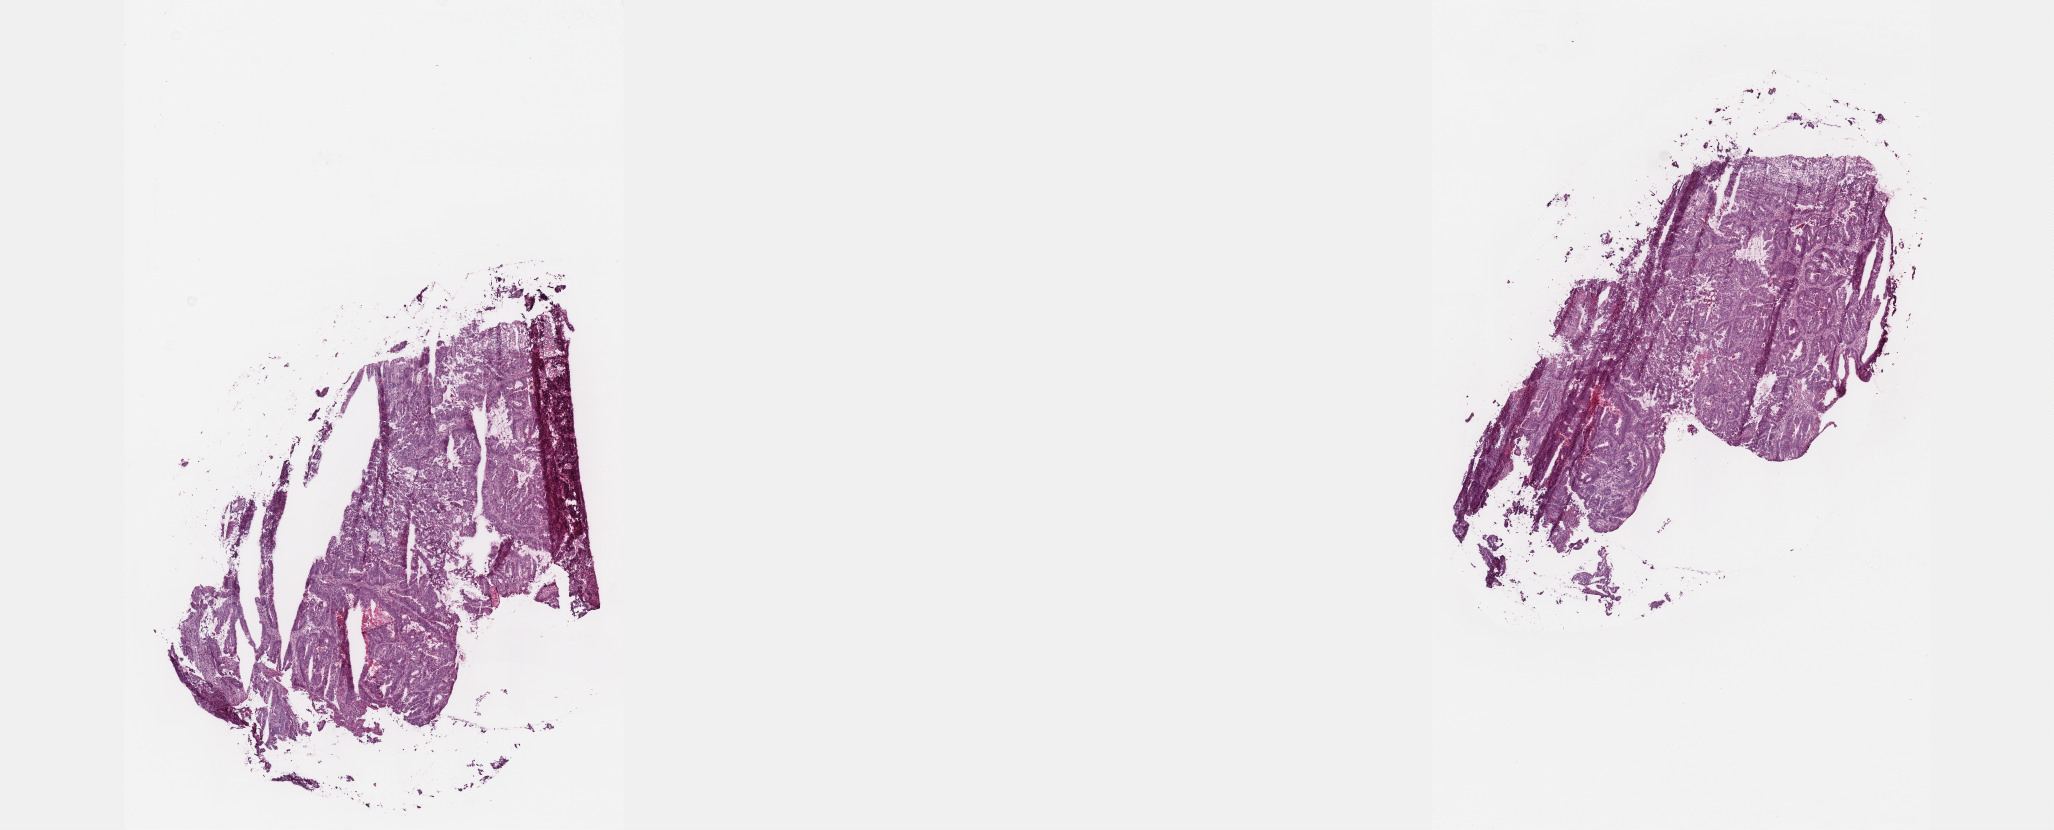
Whole-slide histology image, H&E-stained, low-resolution overview of the scanned area, about 16.6 x 6.7 mm. Frozen section from the top of the tissue portion. Colon, primary tumour sample. Female, age 73 years at initial diagnosis.
Diagnosis: Adenocarcinoma, NOS.